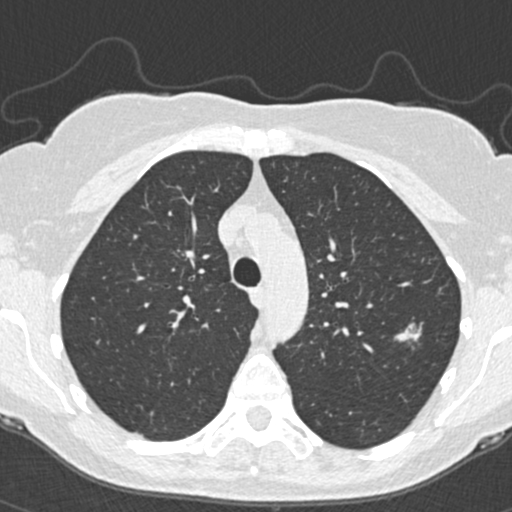
Low-dose screening chest CT, one axial slice. Slice 264 of 350 in the series (ordered by position). Reconstruction kernel B30f. 120 kVp. Lung window (W 1500 / L -600 HU). 1 mm slice thickness. 512 × 512 image matrix.
Annotated regions visible in this slice (outlined manually by an expert reader):
- lesion 1 (tumor, upper lobe of left lung): box from (x=394, y=322) to (x=423, y=342) px